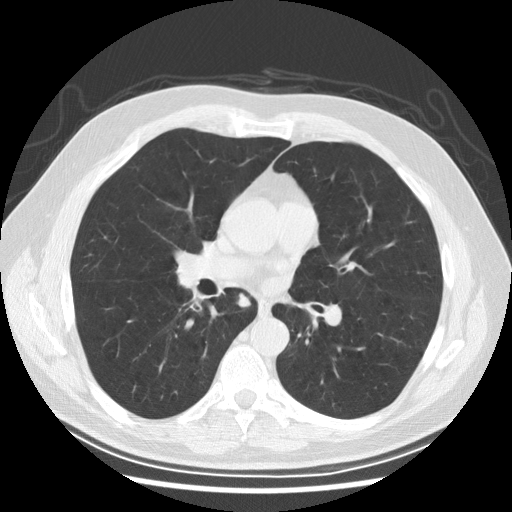
Chest CT (low-dose screening protocol), one axial image; second annual screen; lung window (W 1500 / L -600 HU); 2.5 mm slice thickness; slice 117 of 246 in the series; 512 × 512 image matrix. Male participant, aged 61 years at enrolment. Former smoker at enrolment.
Expert reader's lesion annotation, box from (x=224, y=284) to (x=256, y=317) px. No non-calcified nodule or mass ≥4 mm was recorded by the screening reader at this exam. Lung cancer was diagnosed 382 days after this screen: squamous cell carcinoma, keratinizing, NOS, right lower lobe, stage IIIB (AJCC 6th edition), 40 mm at pathology.